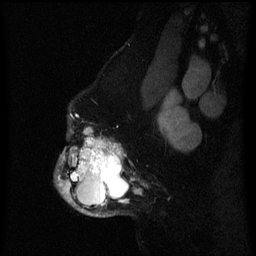
Breast MRI (dynamic contrast-enhanced), one sagittal slice; position 49 of 60 along the scan axis; dynamic contrast-enhanced series, image 2 of 3 at this slice position (ordered by acquisition); 1.5 T; TE 4.2 ms, TR 8 ms; 256 × 256 image matrix, field of view 190 × 190 mm. Patient: female, 50 years.
Structures marked on this image (semi-automatic segmentation, software-assisted and operator-edited):
- analysis volume of interest (the breast-tissue region the enhancement analysis was run in; not a lesion): bounding box [x1, y1, x2, y2] px = [54, 128, 141, 217]
- tumour enhancement mask (voxels above the 70 % enhancement threshold inside the analysis volume of interest): [58, 128, 141, 216]